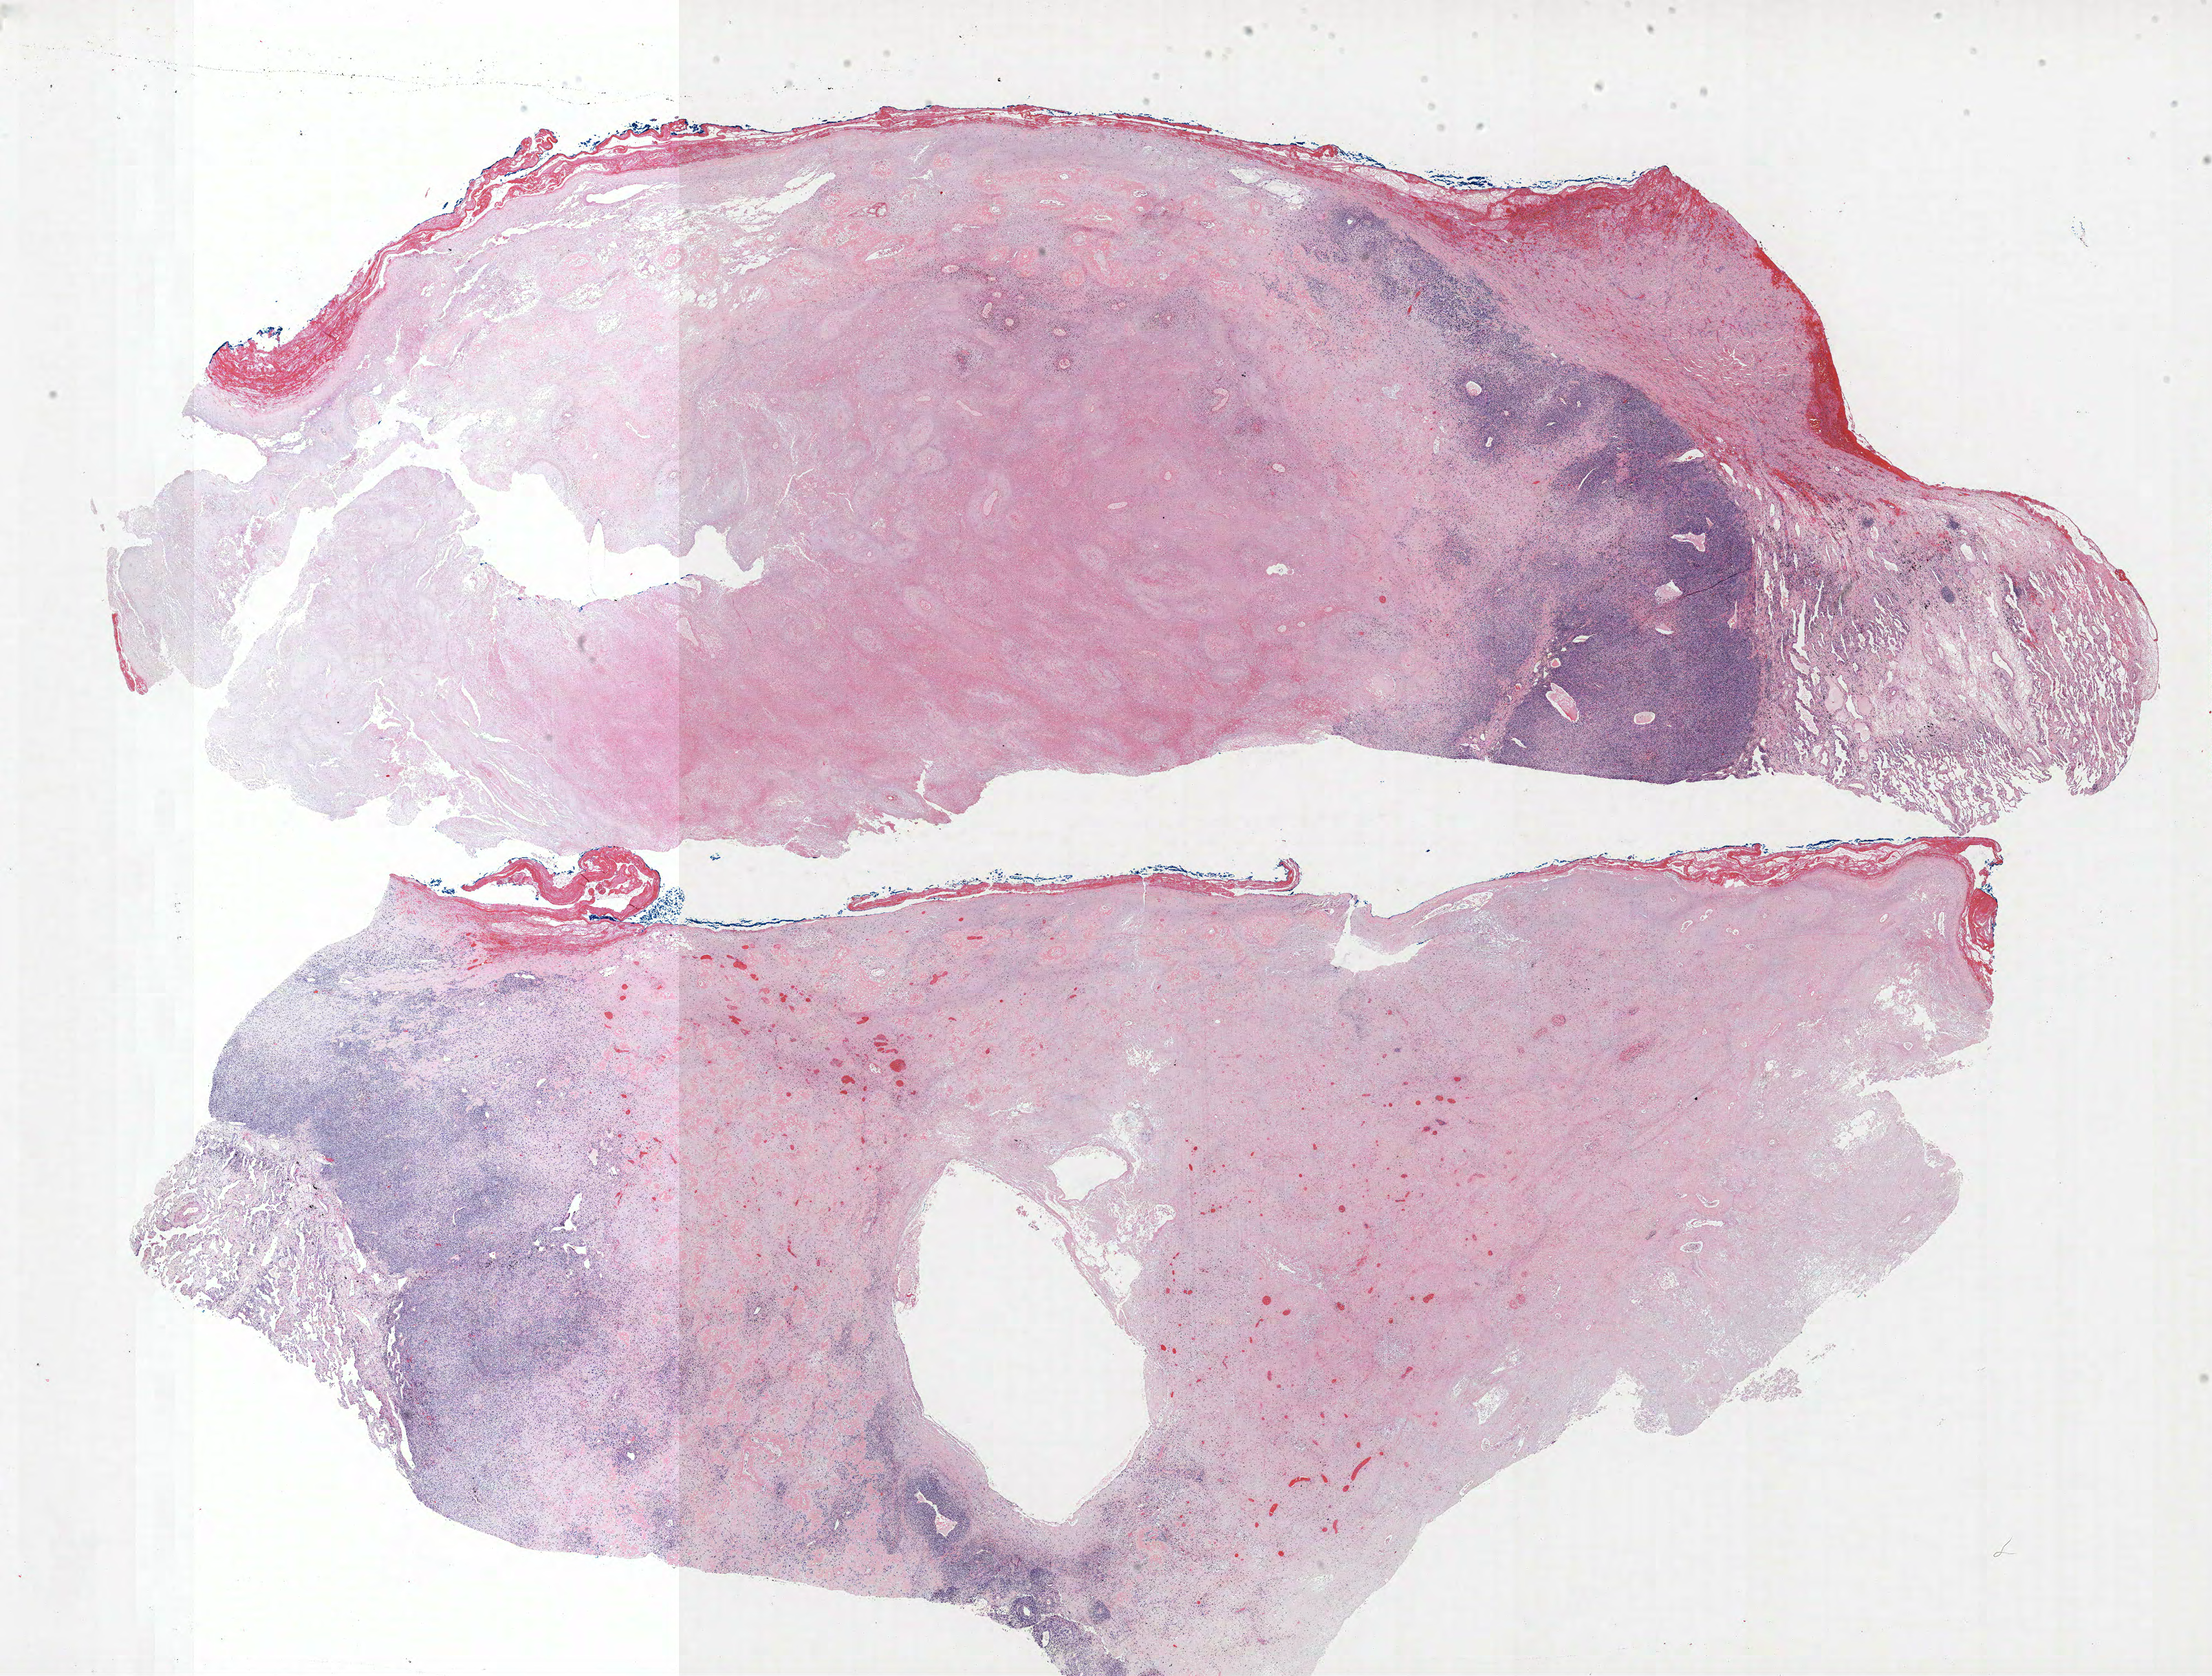
Hematoxylin and eosin (H&E) stained whole-slide image, shown as a low-resolution overview of the whole scanned area (about 27.4 x 20.7 mm), formalin-fixed paraffin-embedded (FFPE) section, lung. Female, age 67 at enrolment. Grade: undifferentiated (G4).
* participant's lung-cancer diagnosis: Pseudosarcomatous carcinoma (ICD-O-3 8033/3)
* primary tumour location (clinical record): right lower lobe
* ICD-O-3 topography: lower lobe of lung (C34.3)
* tumour size (pathology): 135 mm
* stage (AJCC 6th edition): IIIB